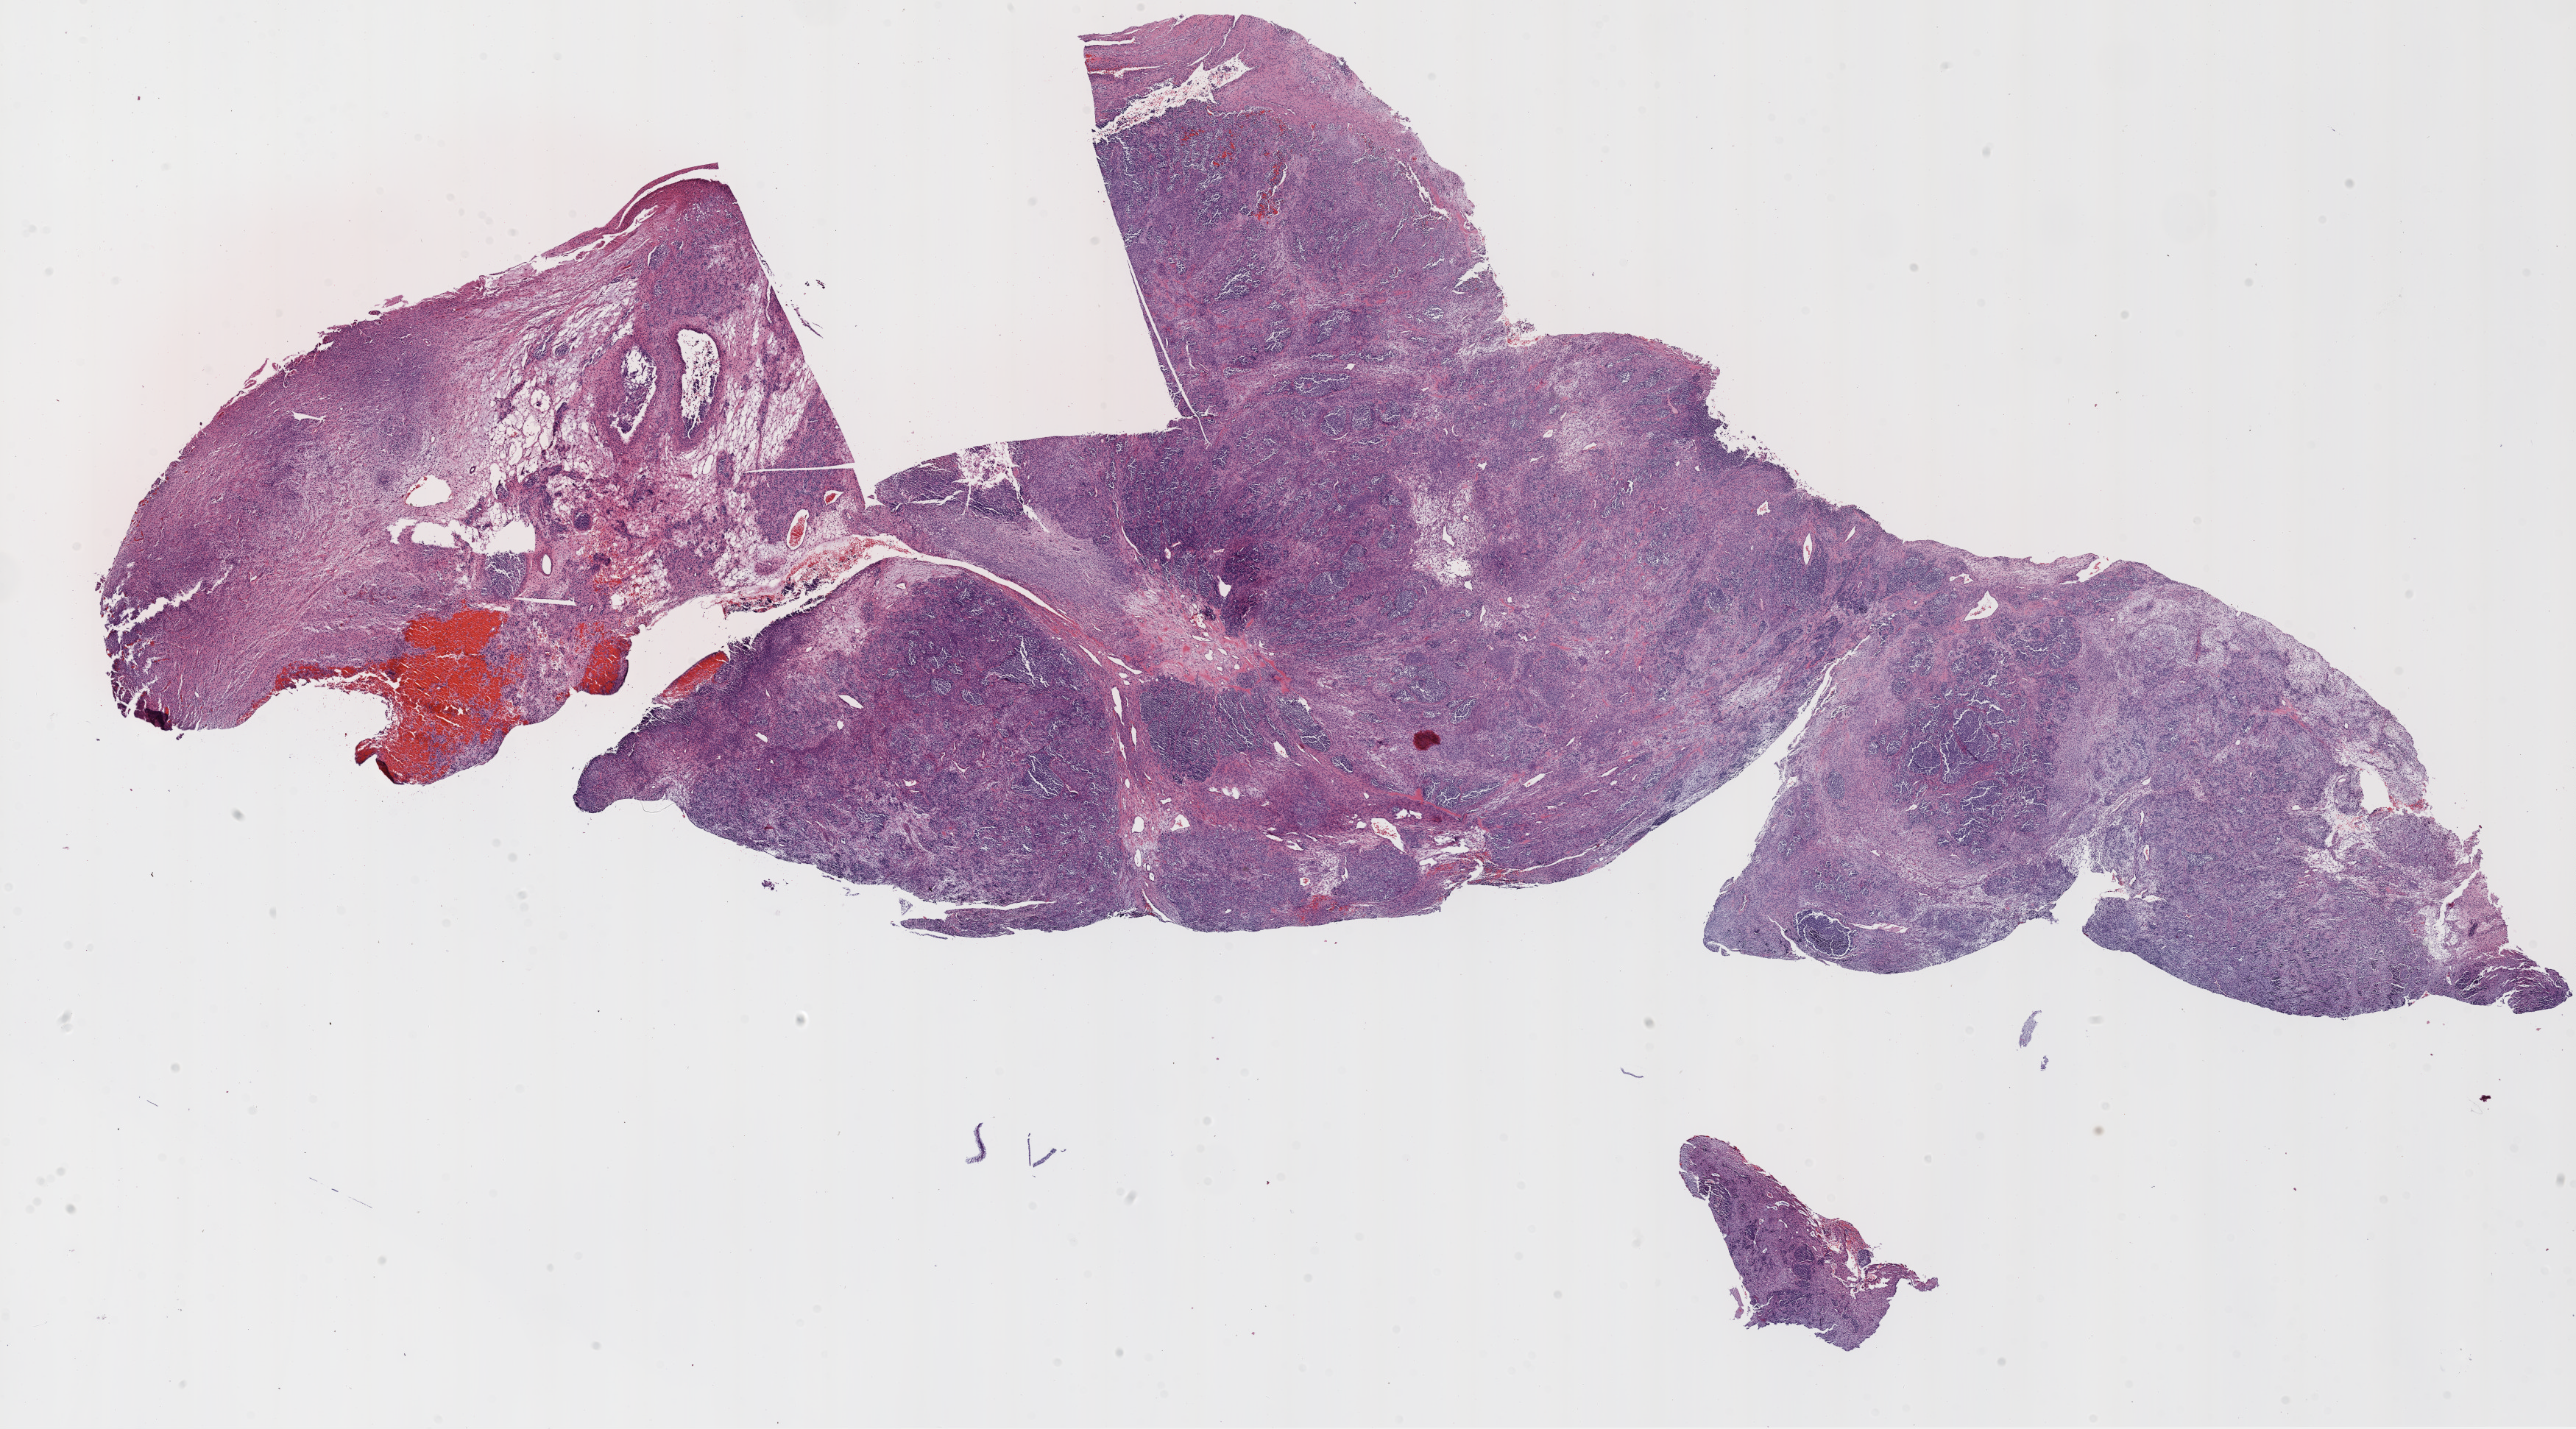
Whole-slide histology image, Hematoxylin and eosin (H&E) stained, a low-resolution overview of the entire scanned area, about 28.1 x 15.6 mm; FFPE section; brain, primary tumour sample. Male, age 42 years at initial diagnosis.
Pathologic diagnosis: Glioblastoma.